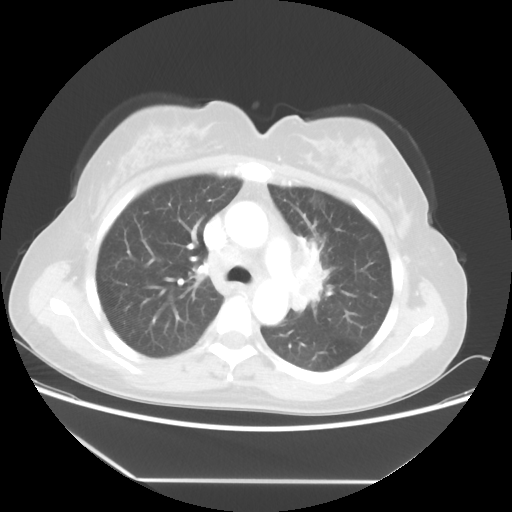
Chest CT, one axial slice; position 35 of 52 along the scan axis; reconstruction kernel STANDARD; 100 kVp; lung window (W 1500 / L -600 HU); 5 mm slice thickness; 512 × 512 image matrix, field of view 390 × 390 mm. Female patient, age 50 years. From the clinical record (not read from this slice): clinical TNM (as recorded): T2 N3 M0.
Outlined on this slice (bounding box drawn by a radiologist):
- lung tumour (recorded histology: adenocarcinoma): bounding box <283,218,331,318> (left, top, right, bottom; pixels)